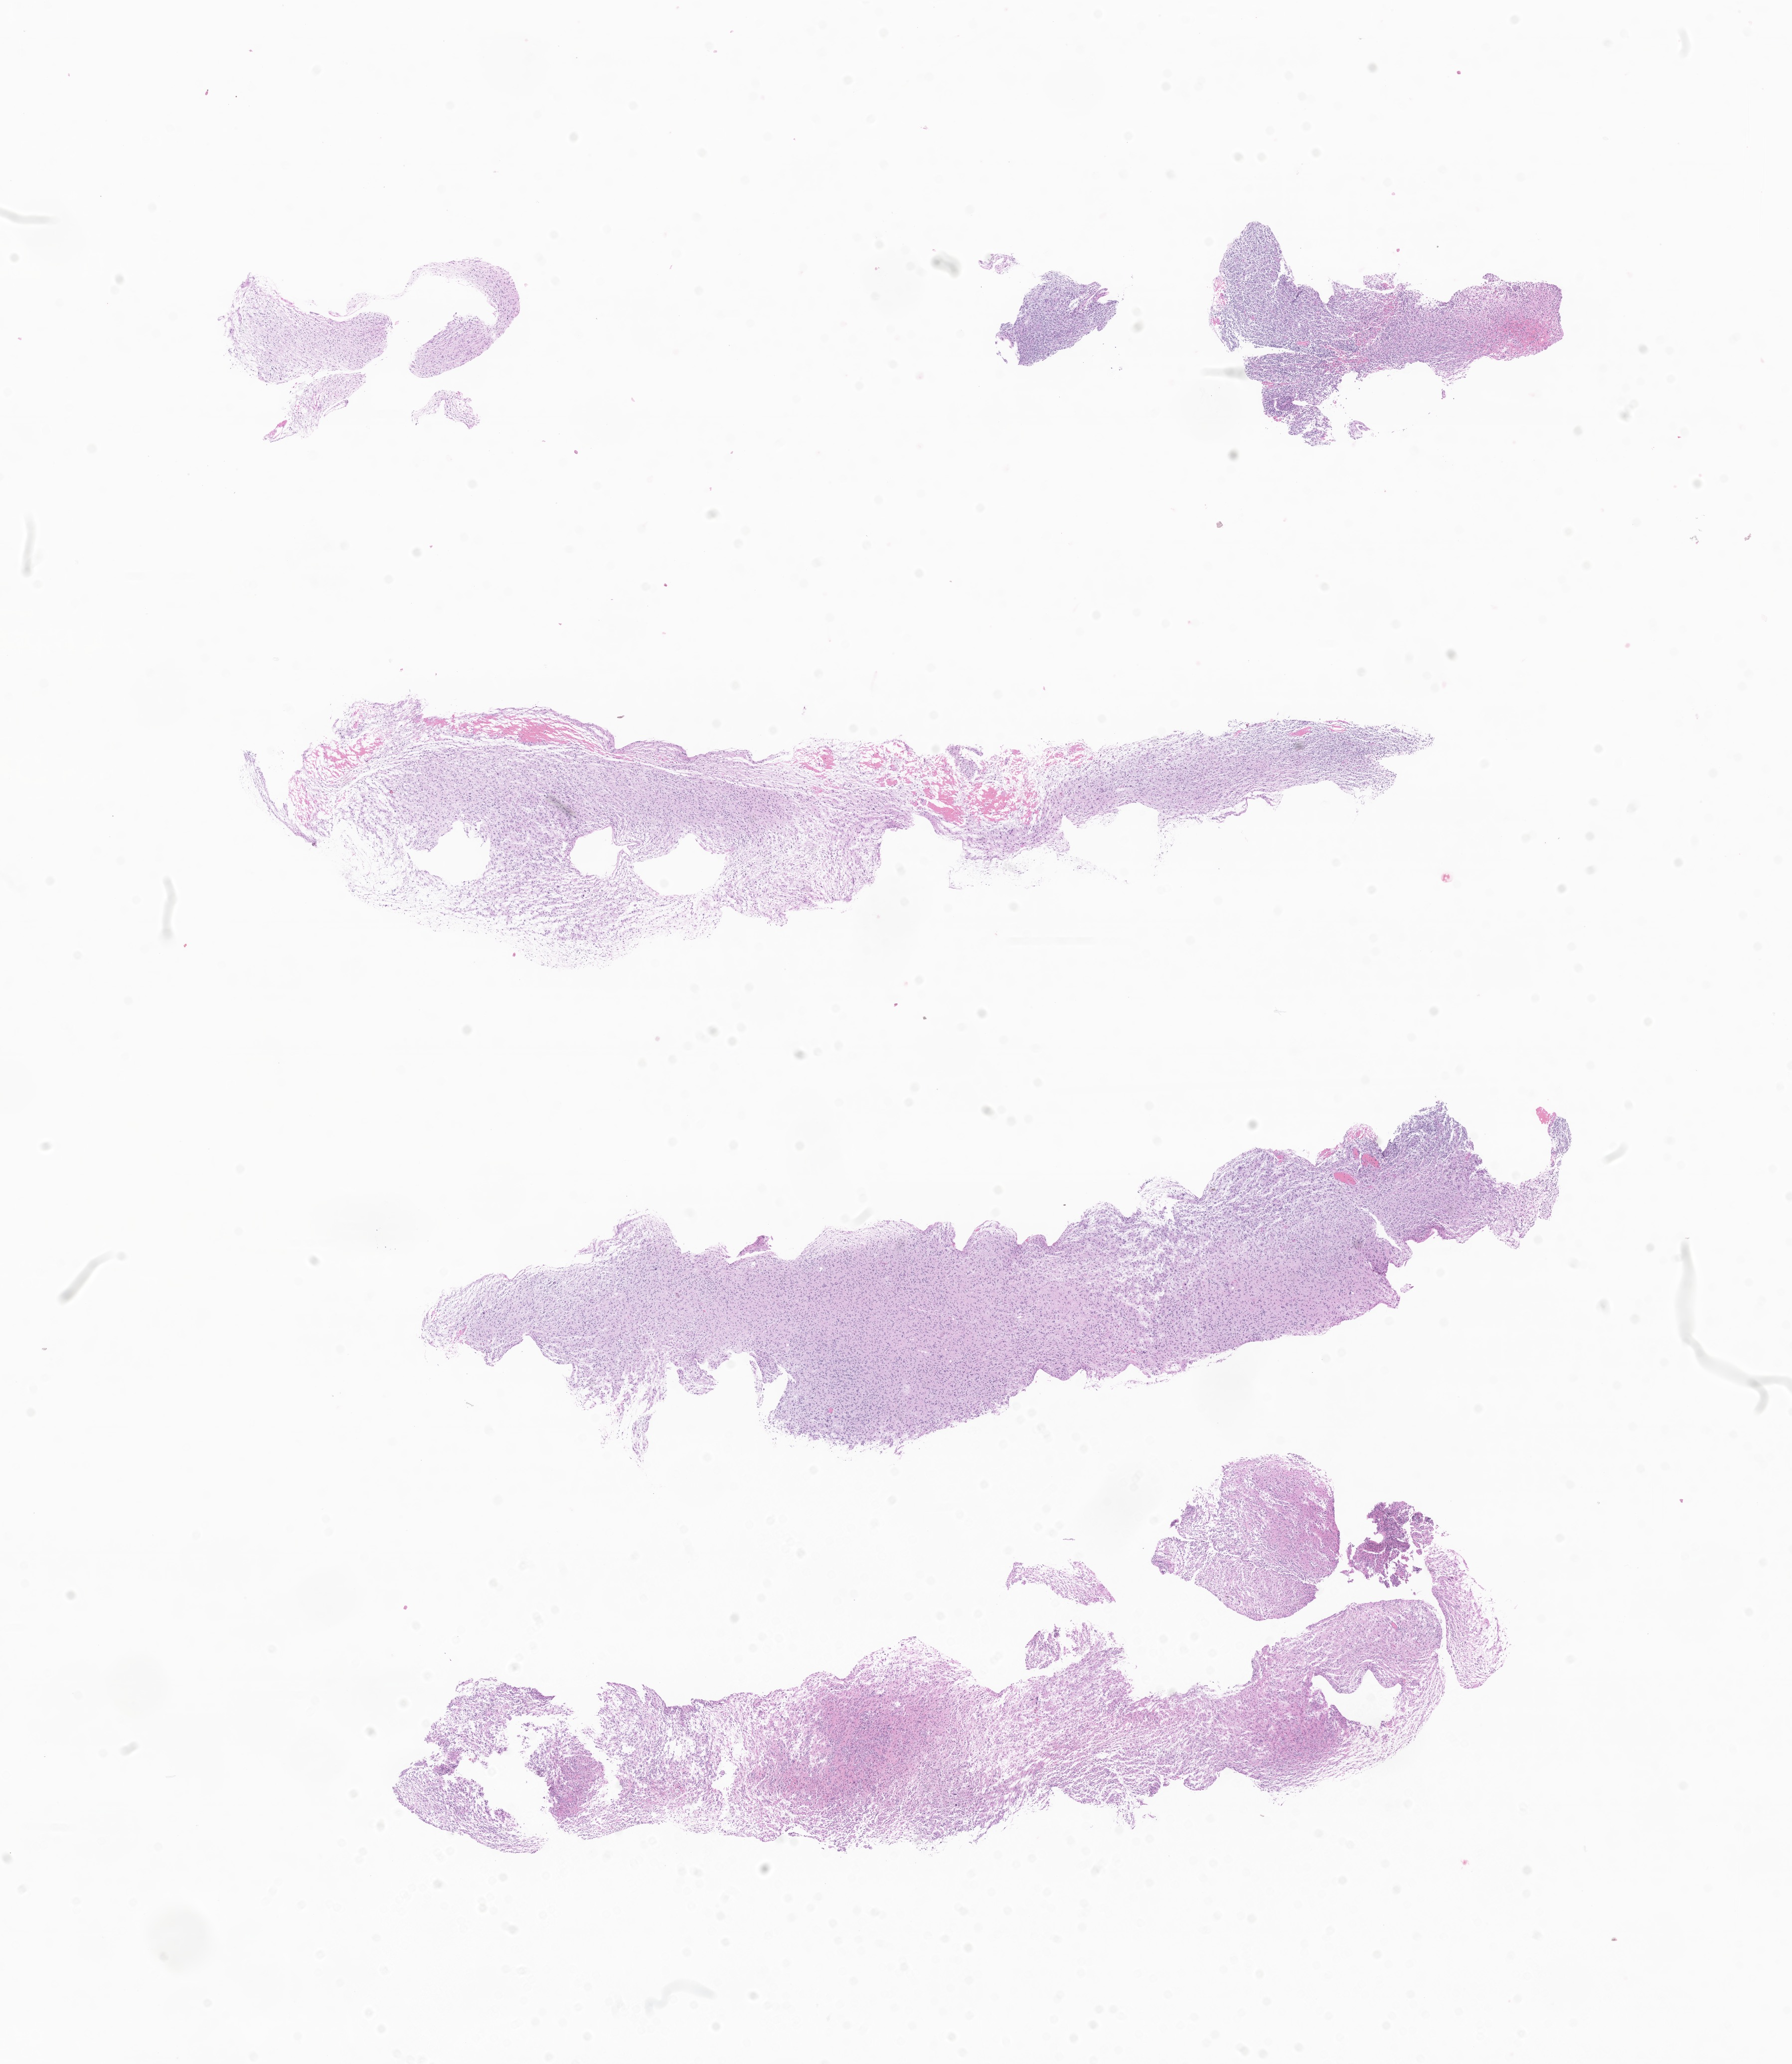
Whole-slide image, H&E stain of tumor tissue from the brain — a low-resolution overview of the entire scanned area, about 15.2 x 17.5 mm, FFPE section. Female patient, age 95 months (7 years 11 months).
Diagnosis: Neoplasm, malignant.